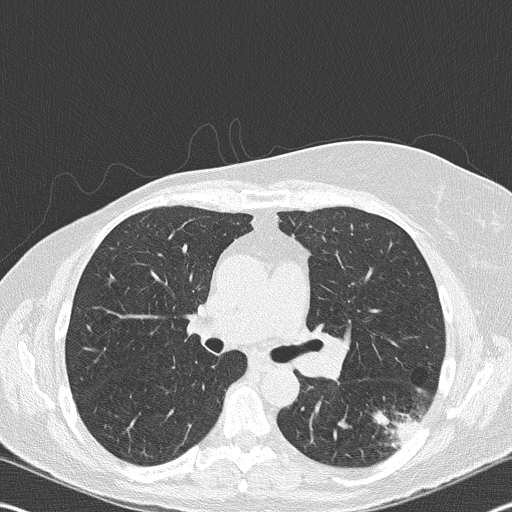
Low-dose screening chest CT, one axial slice; slice 108 of 177 in the series (ordered by position); 120 kVp; lung window (W 1500 / L -600 HU); 2 mm slice thickness; 512 × 512 image matrix.
Outlined on this slice (expert manual segmentation):
- lesion 1 (tumor): bounding box (x1, y1, x2, y2) in pixels: (373, 412, 422, 447)
- lesion 2 (nodule, hilum of left lung): (299, 342, 346, 378)